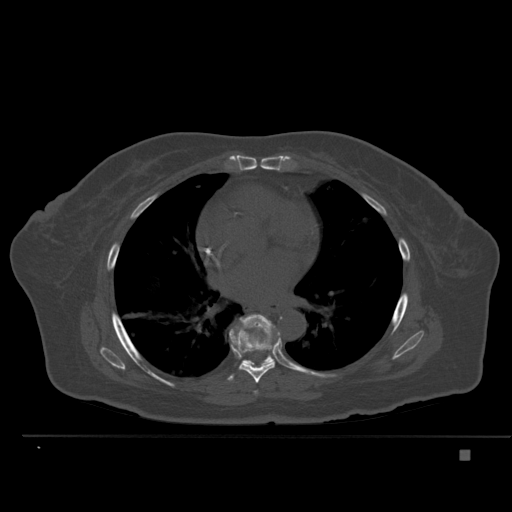
CT including the spine, one axial slice. Position 322 of 477 along the scan axis. Bone window (W 1800 / L 400 HU). 1.5 mm slice thickness. 512 × 512 image matrix. Patient: female, 74 years. Case-level facts recorded for this patient, not image findings: primary cancer: colon.
Structures marked on this image (semi-automatically segmented with operator editing):
- T6 vertebra: bounding box [x1, y1, x2, y2] px = [254, 391, 258, 394]
- T7 vertebra: [227, 324, 280, 383]
- T8 vertebra: [240, 314, 274, 365]